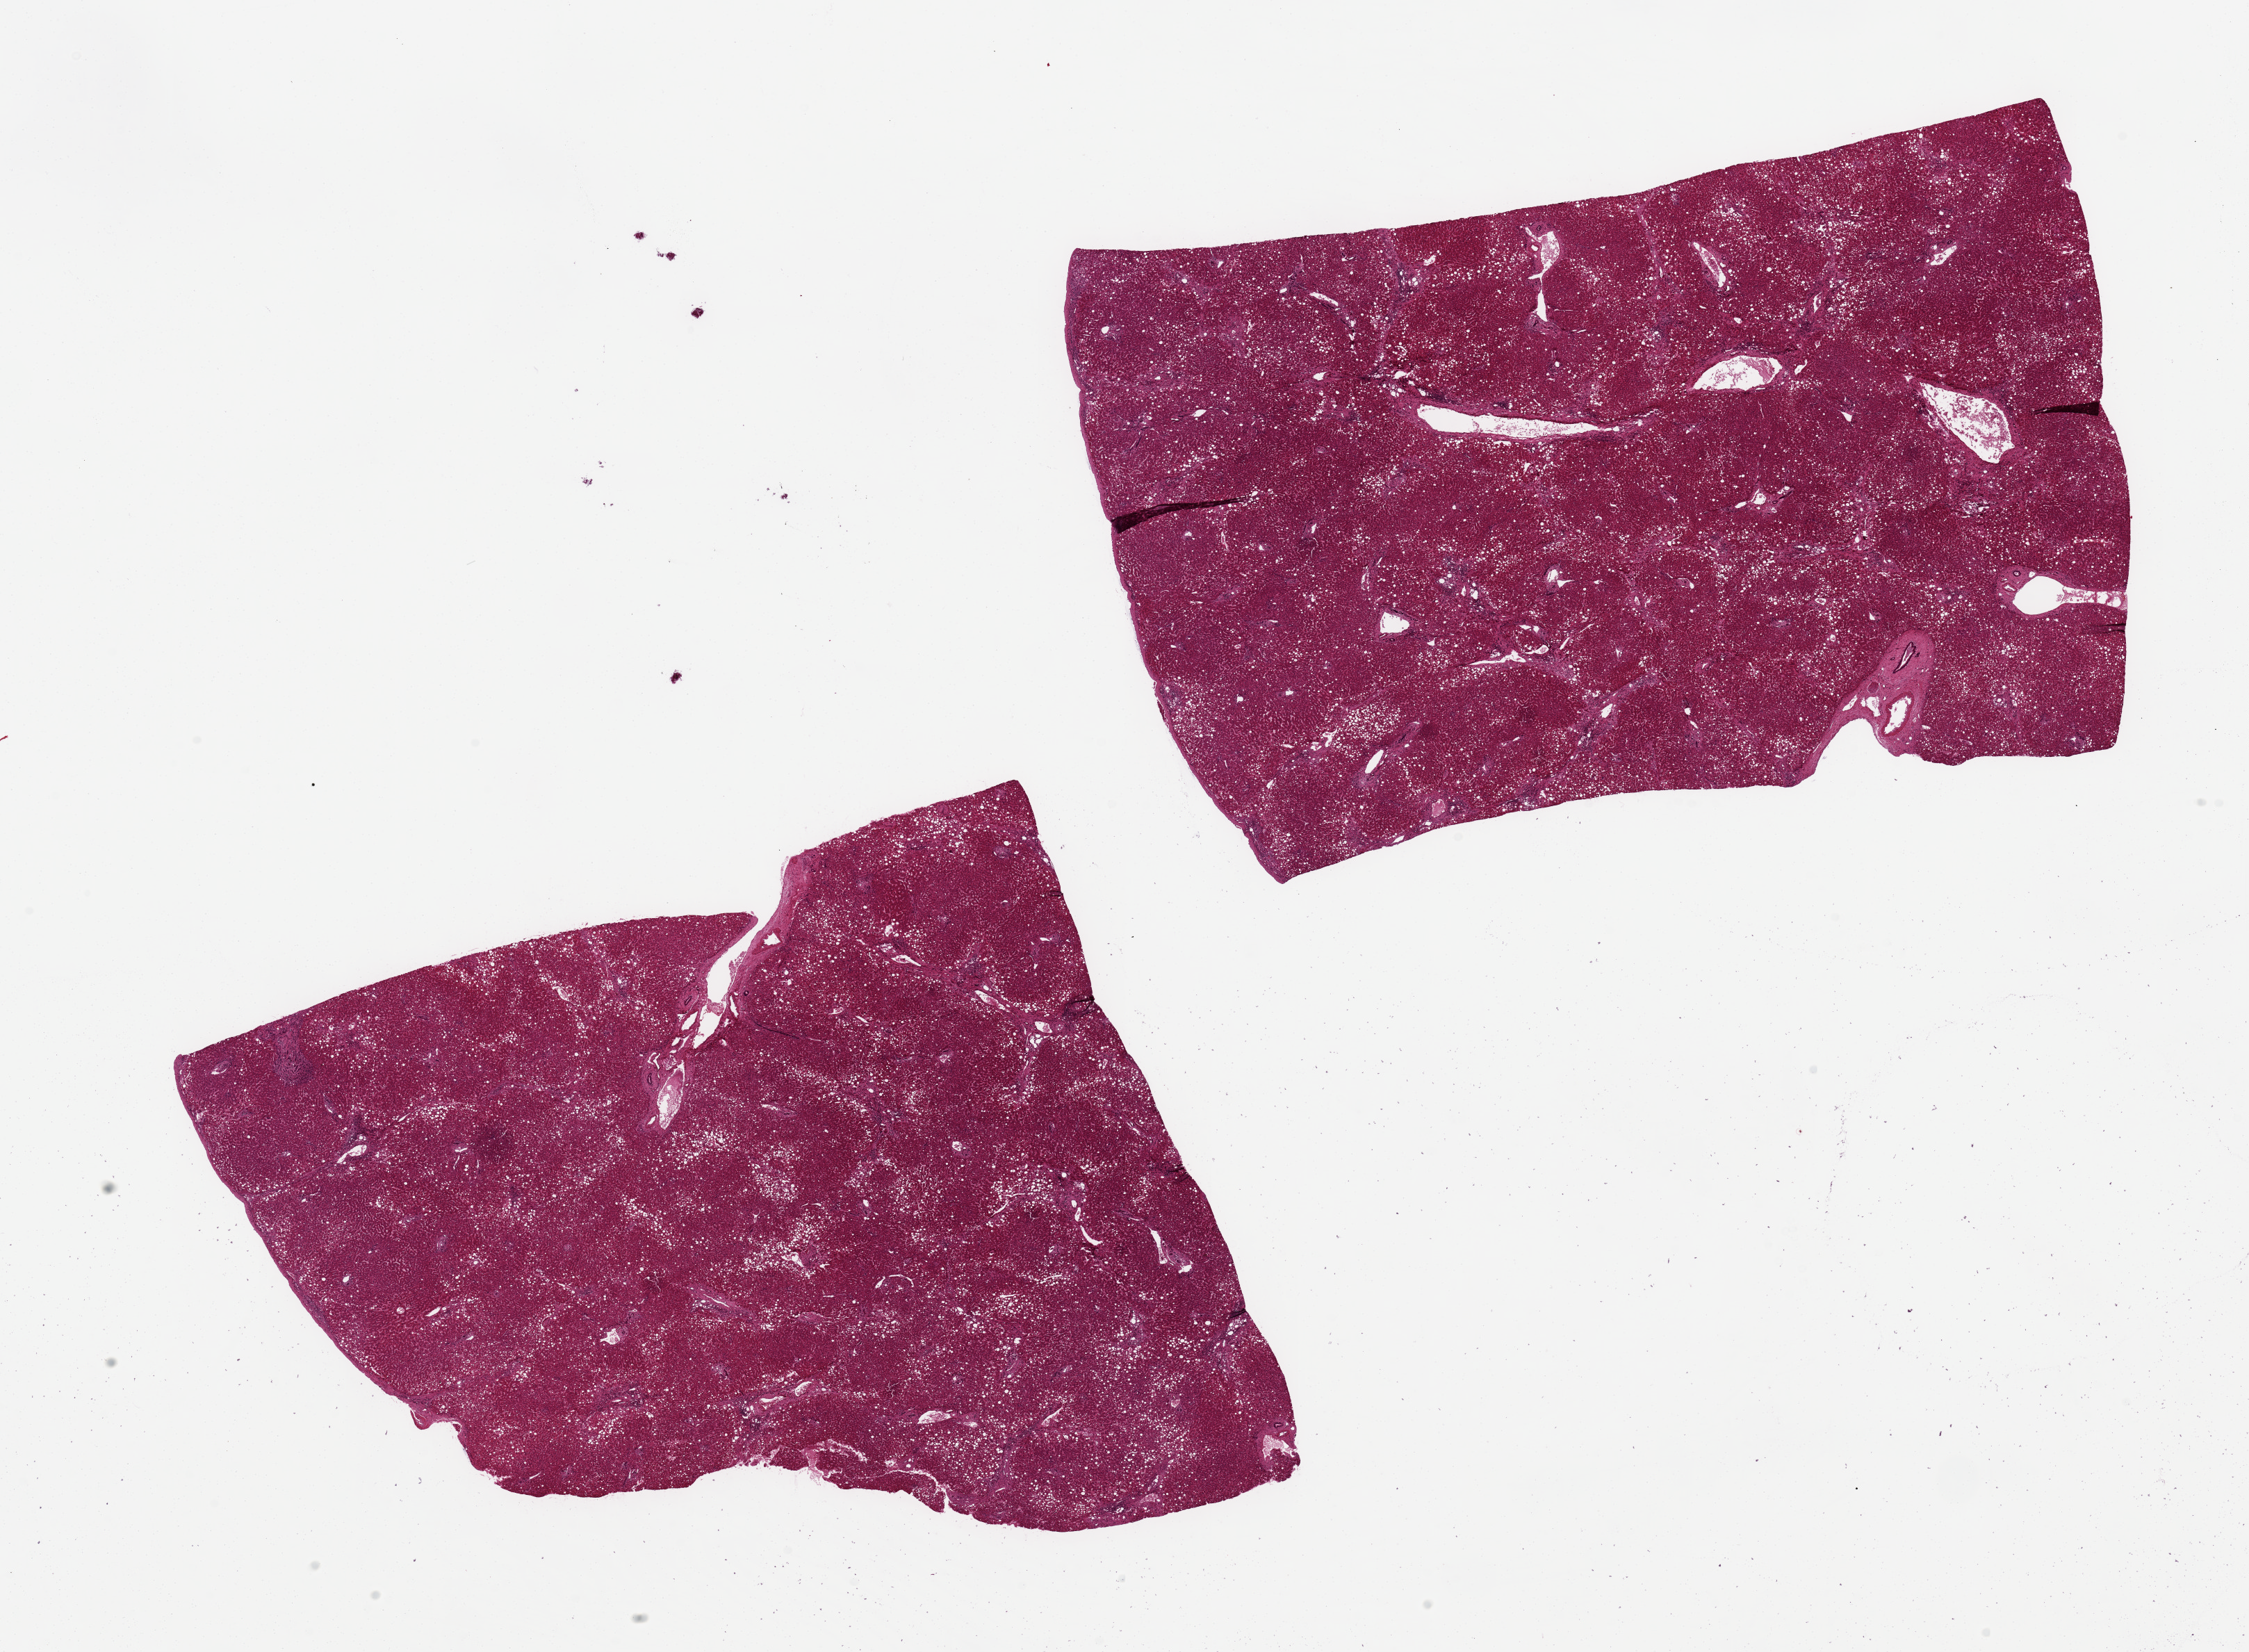
Whole-slide image, hematoxylin and eosin (H&E) stain — low-resolution overview of the scanned area, about 25.6 x 18.8 mm. PAXgene-fixed paraffin-embedded (PFPE) section. Target tissue: liver. Tissue donor sample. Male donor.
- review note (as recorded): 2 pieces 11x8 & 10x8 mm; moderate macrovesicular steatosis; mild microvesicular steatosis